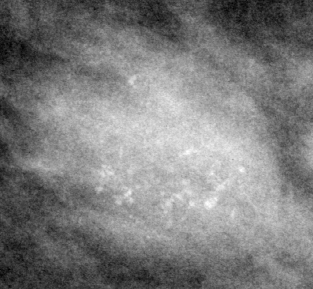
Region of interest cut from a scanned film mammogram (one marked finding); left breast; MLO view.
Finding: calcifications, morphology pleomorphic, distribution clustered; BI-RADS assessment category 4; pathology (as recorded): benign.